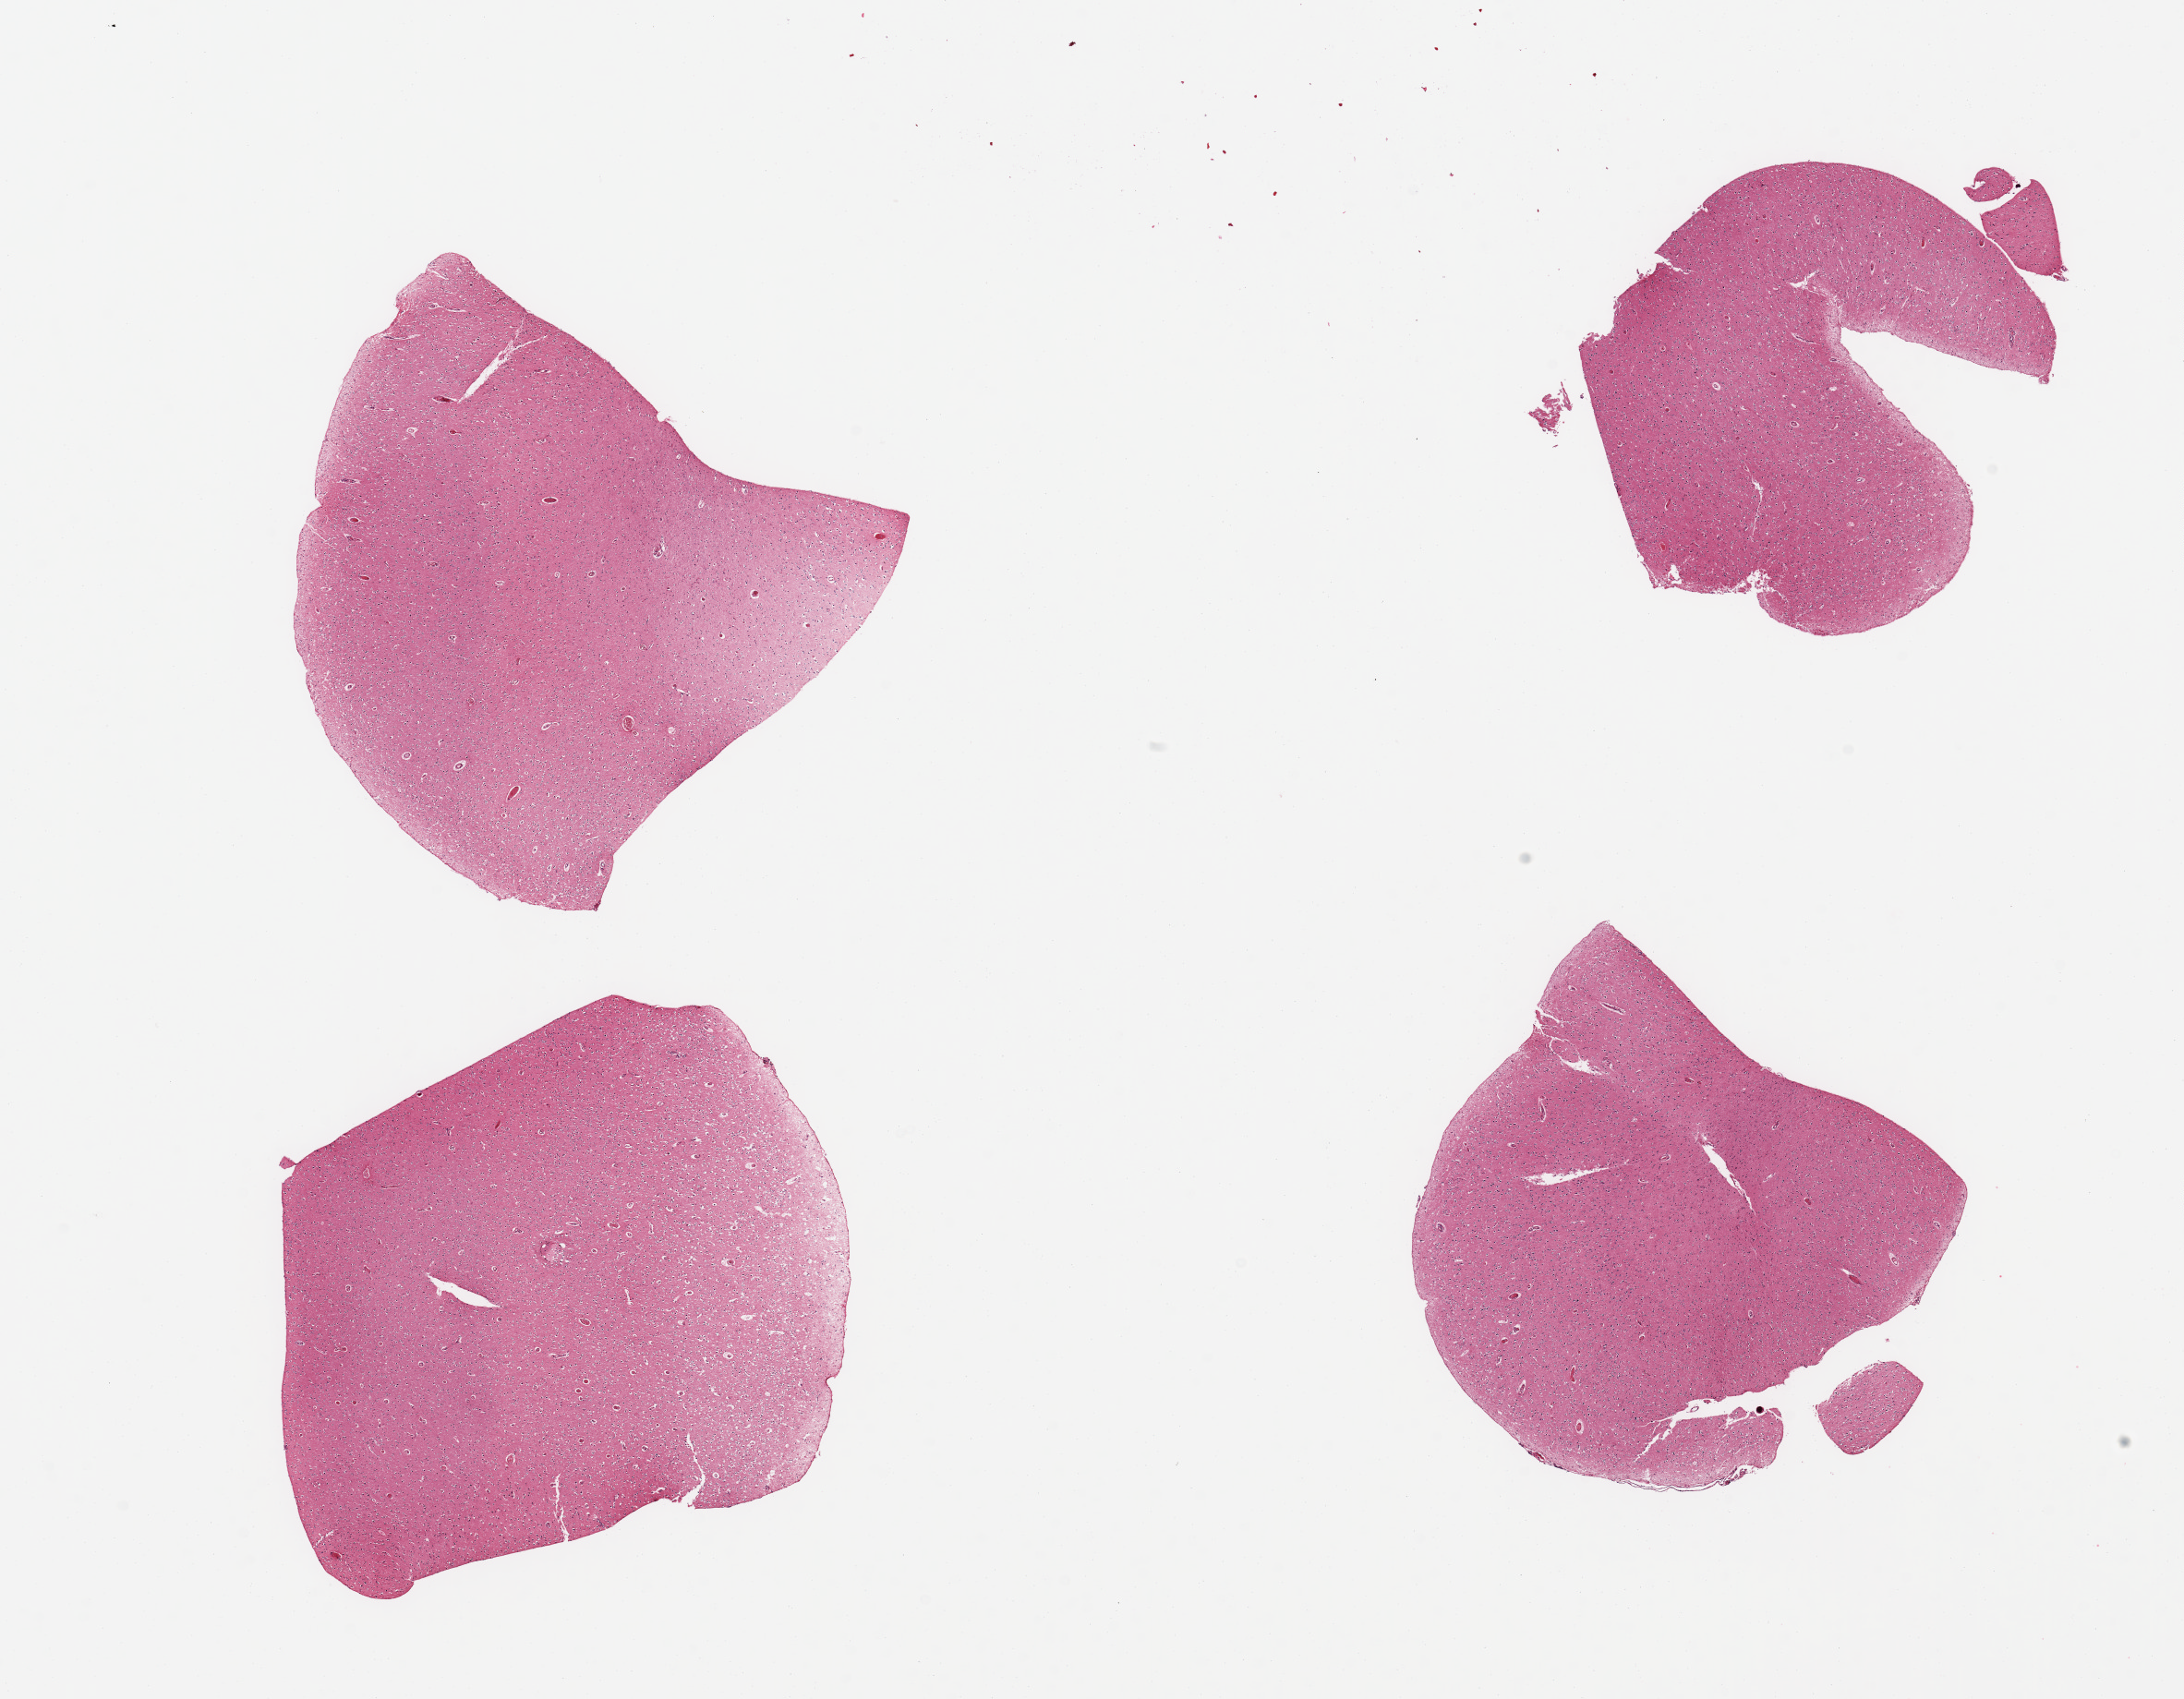
Whole-slide image, haematoxylin and eosin stain, a low-resolution overview of the entire scanned area, about 18.7 x 14.6 mm; PAXgene-fixed paraffin-embedded (PFPE) section; sampled site (target tissue): cerebral cortex; tissue donor sample.
Pathologist's review note for this sample: 4 pieces.